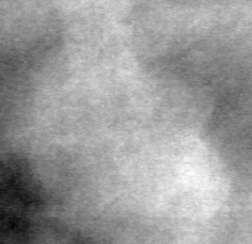
Crop from a digitized film mammogram around one marked abnormality; left breast; MLO view.
Finding: mass, shape oval, margins ill defined; BI-RADS assessment category 4; pathology (as recorded): benign.